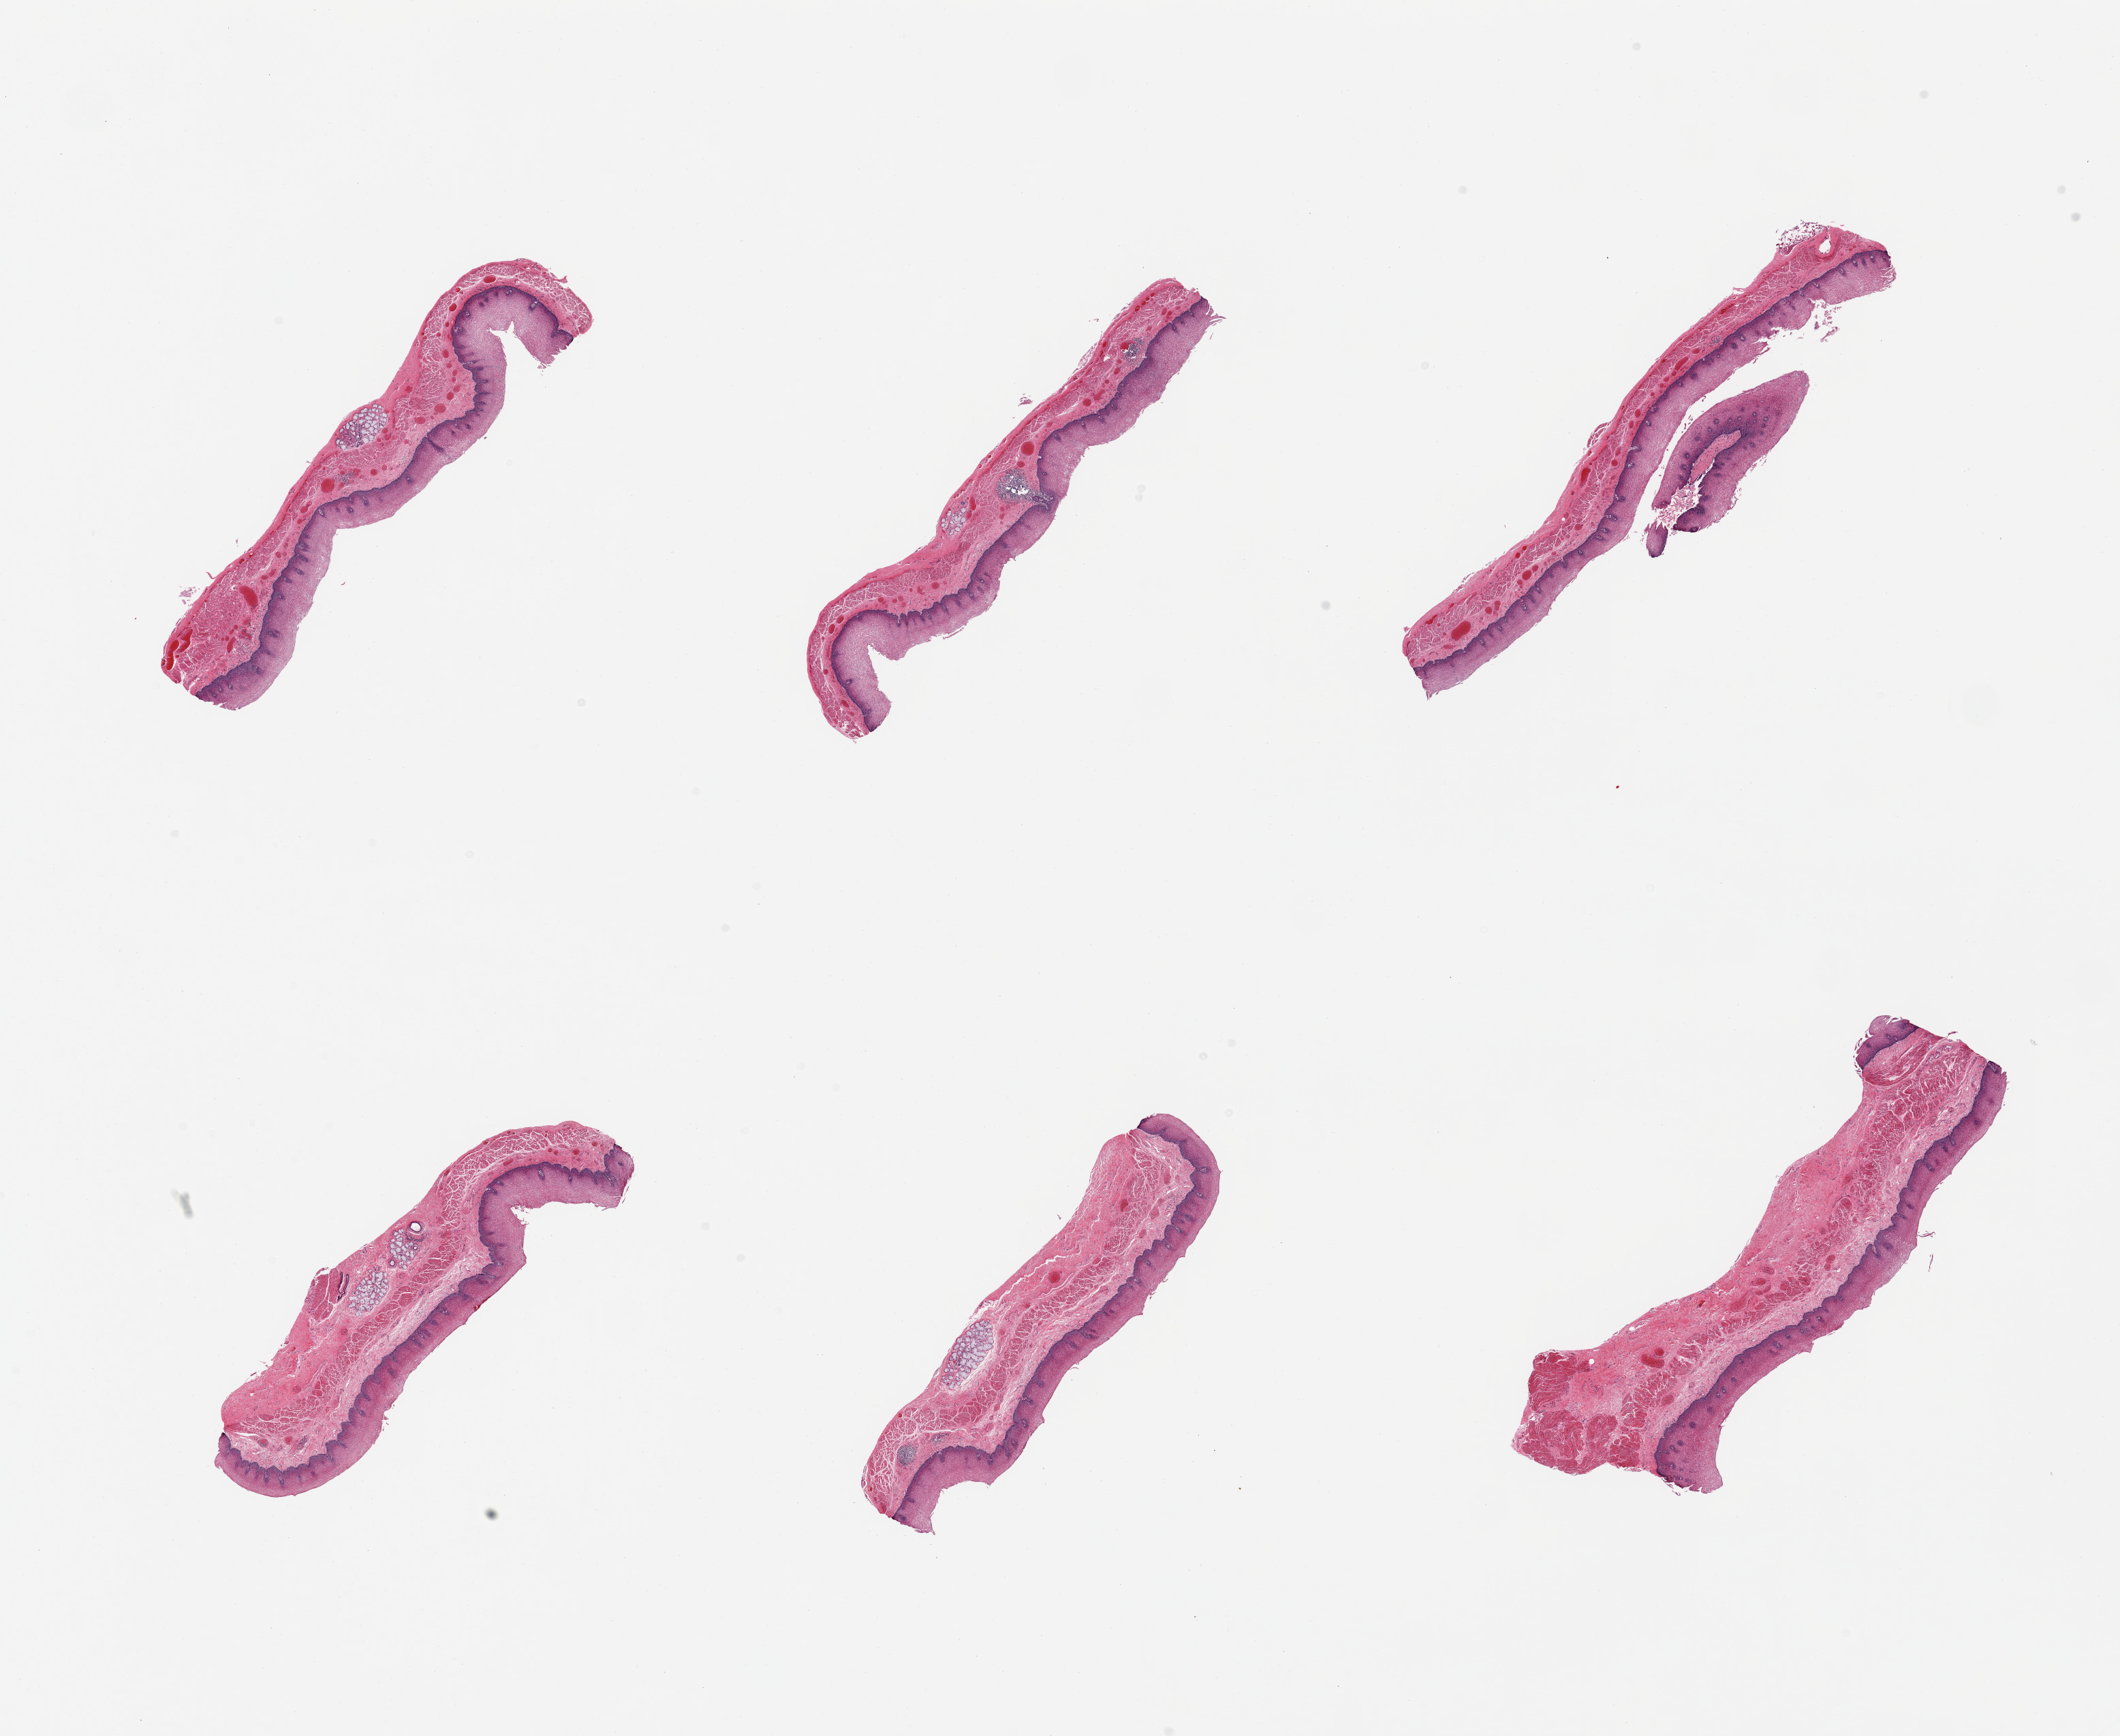
Haematoxylin and eosin whole-slide image, brightfield — shown as a low-resolution overview of the whole scanned area (about 24.6 x 20.2 mm); PAXgene-fixed paraffin-embedded (PFPE) section; sampled site (target tissue): esophageal mucous membrane; tissue donor sample. Donor: male.
Review note (as recorded): 6 pieces; 1 focus of chronic inflammation.